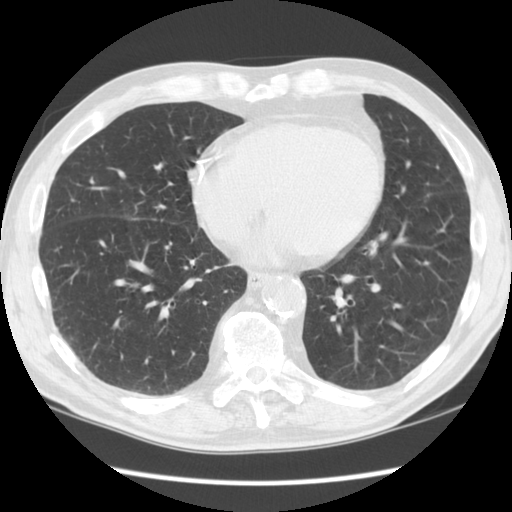
Chest CT (low-dose screening protocol), one axial image; second screening round (one year after baseline); lung window (W 1500 / L -600 HU); 2.5 mm slice thickness; standard (soft-tissue) reconstruction kernel (STANDARD); slice 84 of 132 in the series. Male, age 64 years at enrolment. Current smoker at enrolment.
Expert-annotated lung lesion, bounding box [x1, y1, x2, y2] px = [130, 194, 178, 233]. Reader record for this screening exam (exam-level; its link to the box is not recorded): non-calcified nodule or mass ≥4 mm, right middle lobe, 6 × 5 mm, smooth margins, soft tissue attenuation, pre-existing on the prior screen: no. Lung cancer was diagnosed 300 days after this screen (after the third annual screen): non-small cell carcinoma, right middle lobe, poorly differentiated (G3), stage IIIA (AJCC 6th edition), 20 mm at pathology.